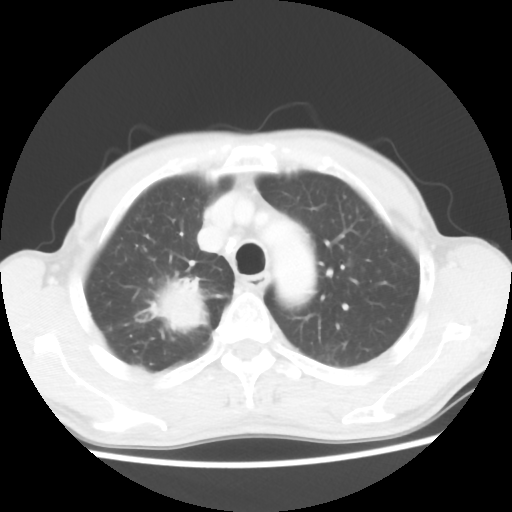
Chest CT, one axial slice. Position 41 of 52 along the scan axis. Reconstruction kernel STANDARD. 100 kVp. Lung window (W 1500 / L -600 HU). 5 mm slice thickness. 512 × 512 image matrix. Patient: male, 66 years. From the clinical record (not read from this slice): clinical TNM (as recorded): T2 N0 M1a.
Outlined on this slice (rectangle marked by the reading radiologist):
- lung tumour (recorded histology: adenocarcinoma): bounding box [x1, y1, x2, y2] px = [130, 267, 222, 337]